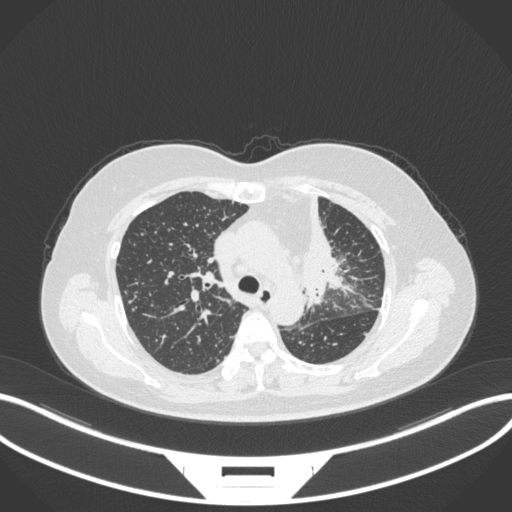
Chest CT, one axial slice. Position 232 of 348 along the scan axis. Reconstruction kernel B31f. Lung window (W 1500 / L -600 HU). 512 × 512 image matrix, field of view 400 × 400 mm. Patient: female, 49 years. From the clinical record (not read from this slice): clinical TNM (as recorded): T1c N0 M1.
Structures marked on this image (bounding box drawn by a radiologist):
- lung tumour (recorded histology: adenocarcinoma): bounding box [x1, y1, x2, y2] px = [290, 186, 349, 306]